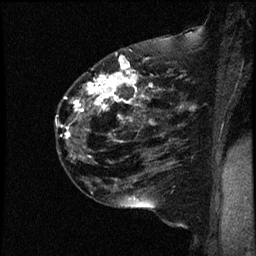
Breast MRI (dynamic contrast-enhanced), one sagittal slice. Slice 32 of 44 in the series (ordered by position). Dynamic contrast-enhanced study with each time point stored as its own series, time point 2 of 4 at this slice position (early post-contrast, ordered by acquisition time). 1.5 T. TE 4.2 ms, TR 17.7 ms. 2 mm slice thickness. 256 × 256 image matrix, field of view 200 × 200 mm. Patient: female, 52 years. Case-level facts recorded for this patient, not image findings: setting: breast cancer imaged before/during neoadjuvant chemotherapy; receptor status: HR-positive, HER2-negative.
Structures marked on this image (semi-automatically segmented with operator editing):
- analysis volume of interest (the breast-tissue region the enhancement analysis was run in; not a lesion): bounding box [x1, y1, x2, y2] px = [55, 48, 163, 147]
- tumour enhancement mask (voxels above the 100 % enhancement threshold inside the analysis volume of interest): [57, 53, 156, 139]